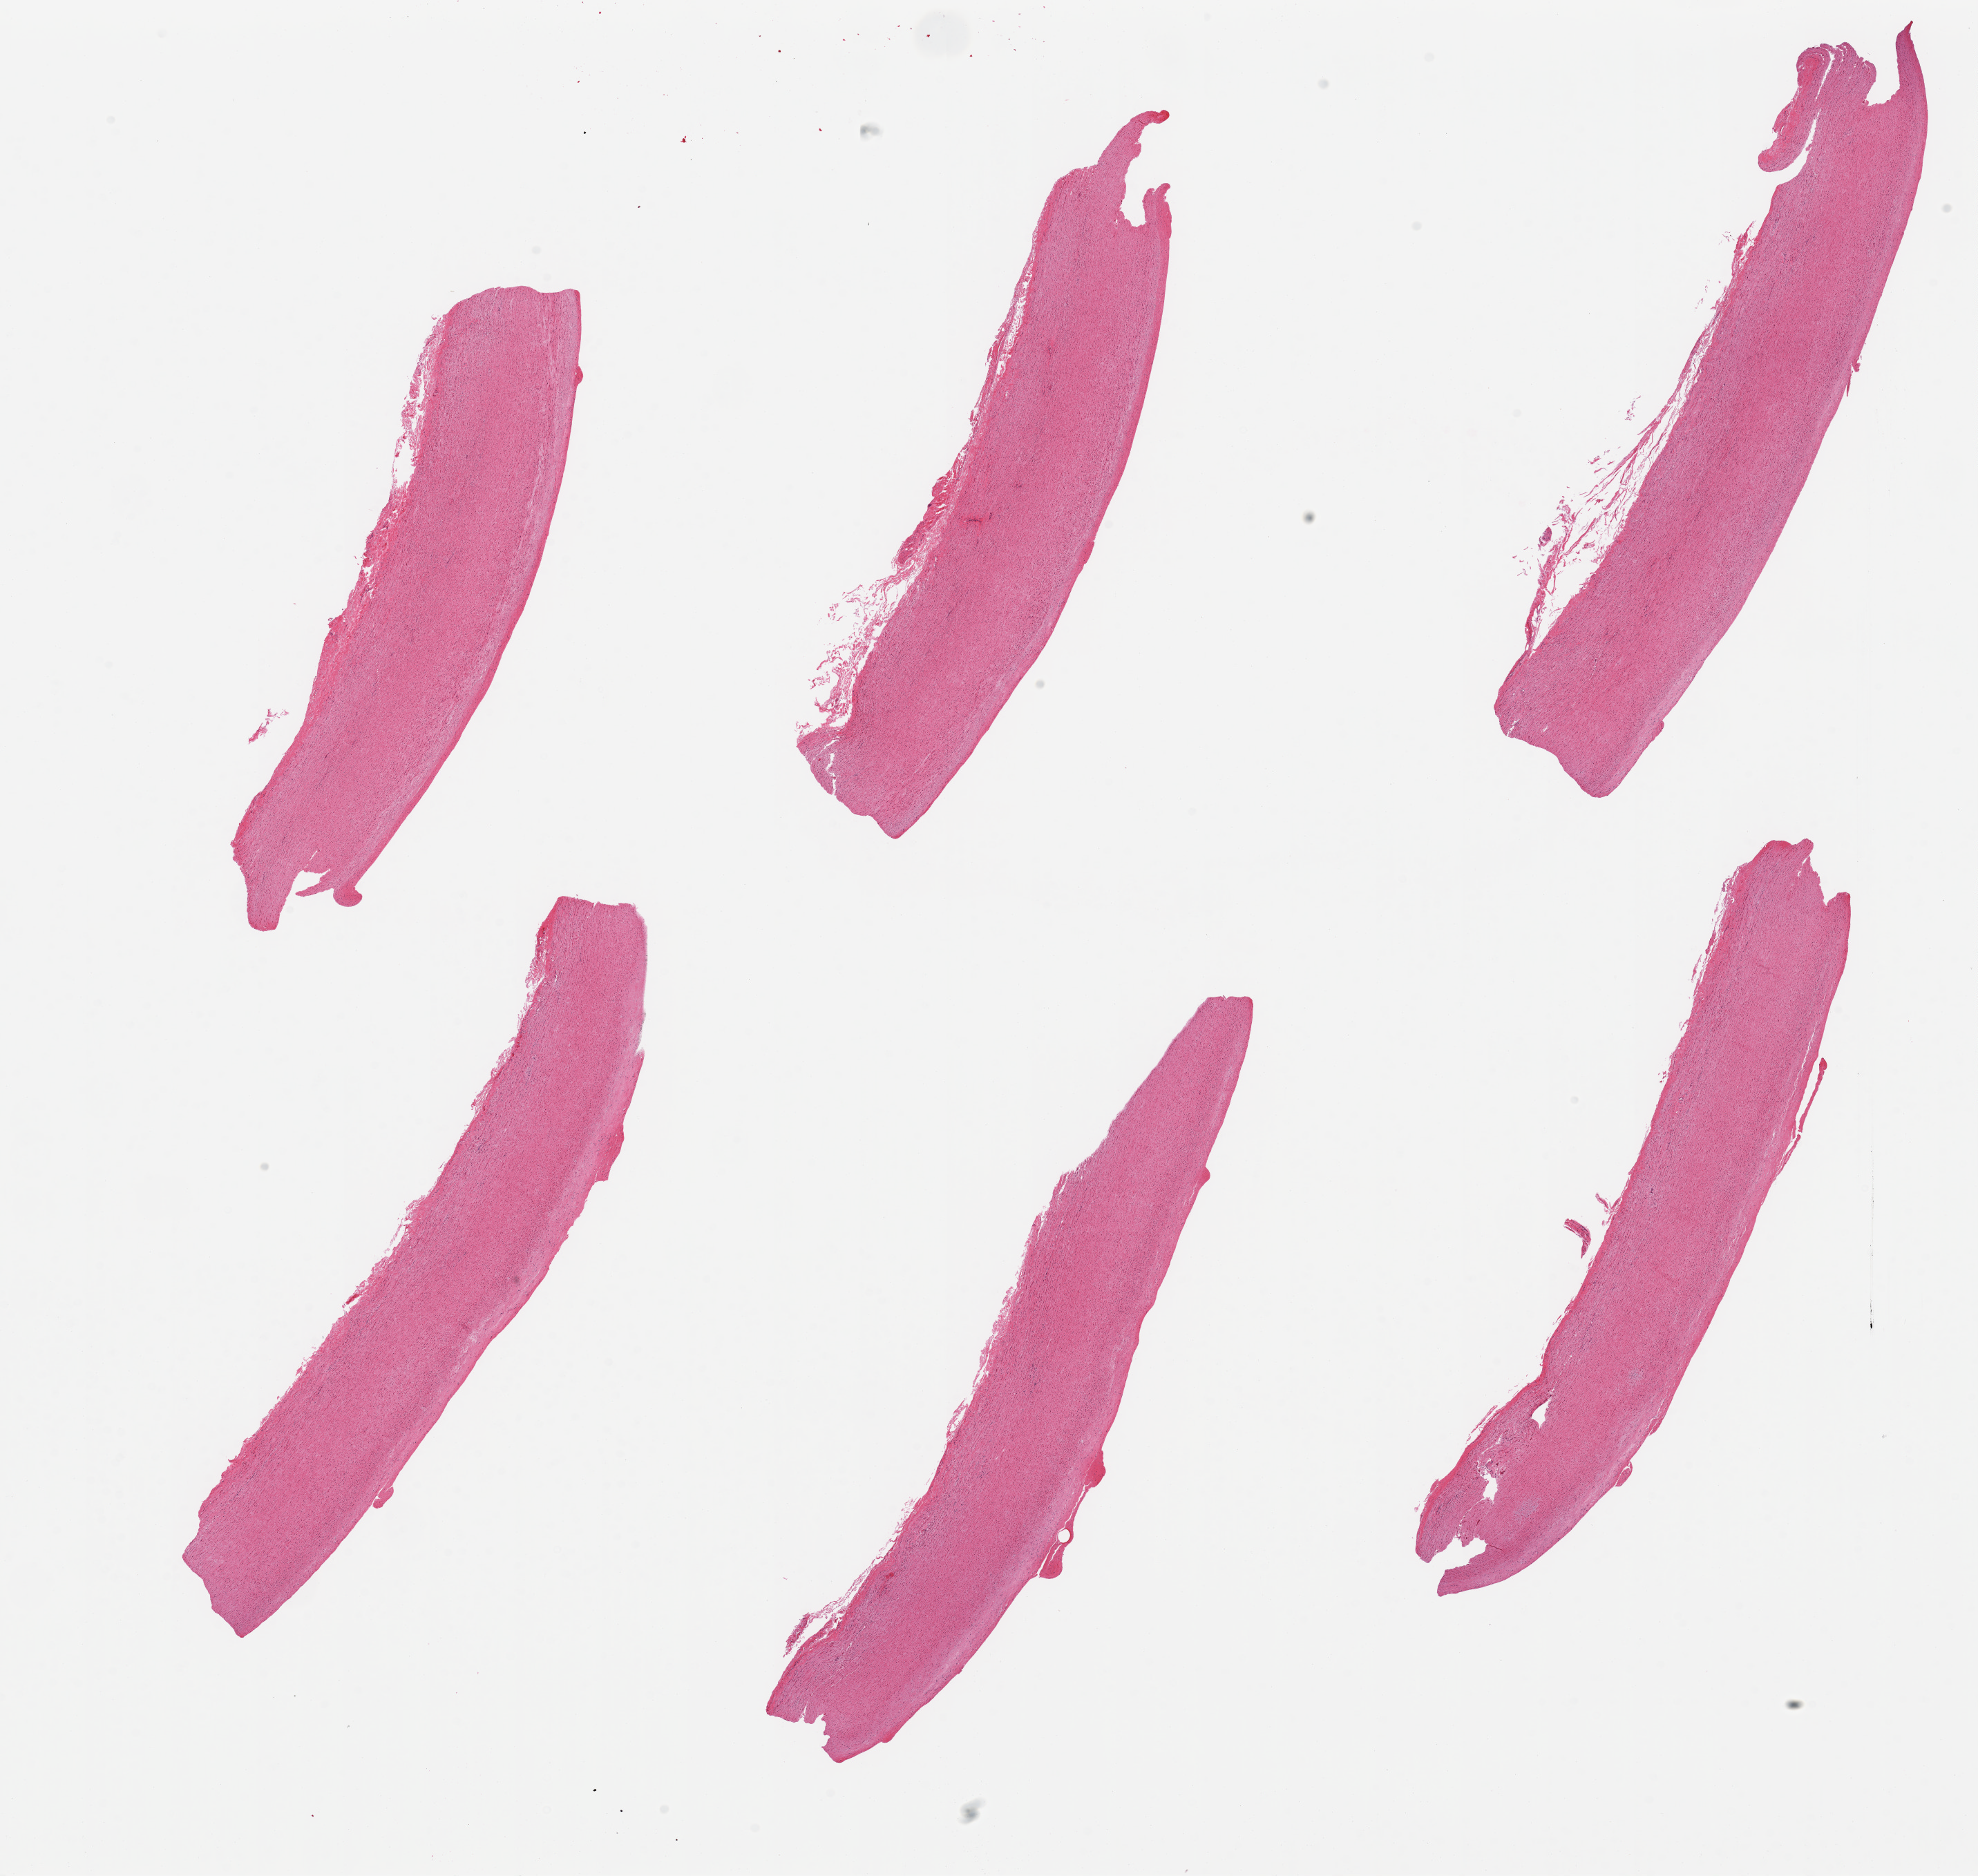
Haematoxylin and eosin whole-slide image, a low-resolution overview of the entire scanned area, about 22.6 x 21.5 mm (from a 20x scan); PAXgene-fixed, paraffin-embedded tissue; section of aorta (target tissue); tissue donor sample. Donor sex: male.
Pathologist's review note for this sample: 6 pieces; focal intimal plaques; well trimmed.